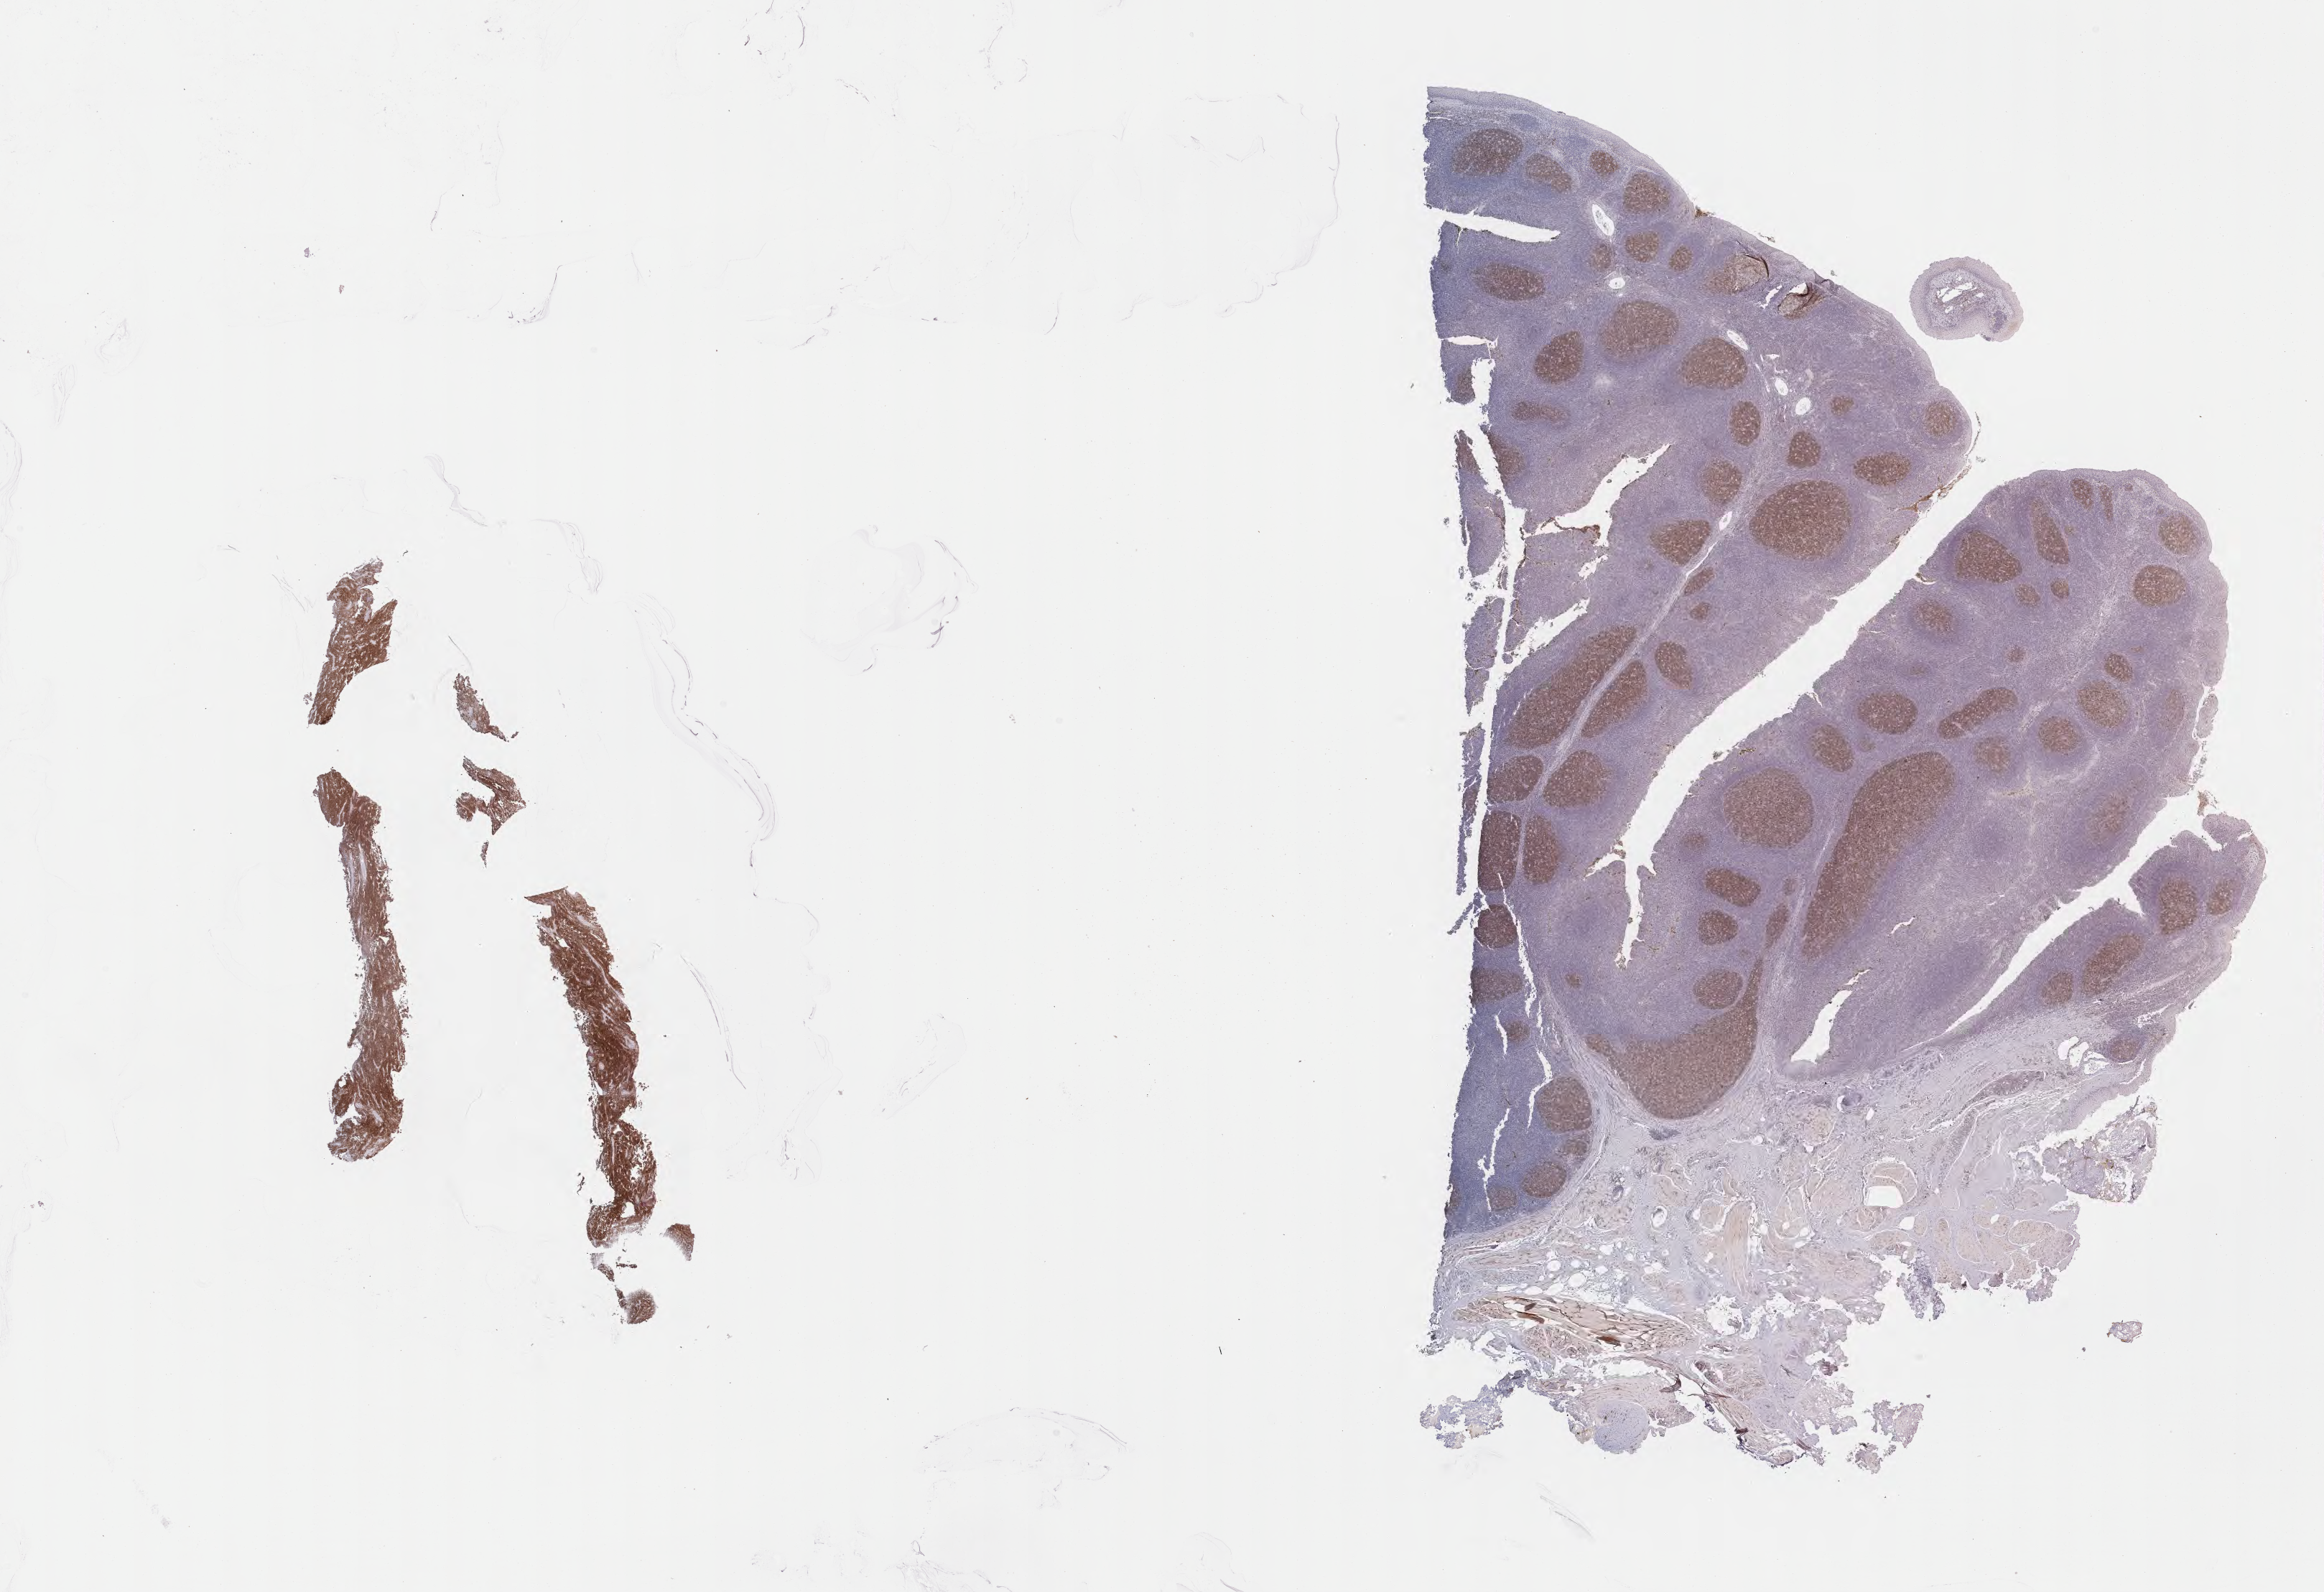
IHC for CD10, whole-slide image, whole scanned area (about 26.2 x 17.9 mm) shown as a low-resolution overview, tumor tissue, site: spleen. Male, age 6 years at initial diagnosis.
Diagnosis: Burkitt lymphoma, NOS.